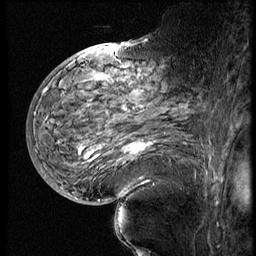
Breast MRI (dynamic contrast-enhanced), one sagittal slice. 4 images stored at this slice position (order not interpretable as contrast timing). 1.5 T. TE 4.2 ms, TR 9 ms. 2.5 mm slice thickness. 256 × 256 image matrix. Female patient, age 56 years. From the clinical record (not read from this slice): setting: breast cancer imaged before/during neoadjuvant chemotherapy; receptor status: HER2-positive.
Annotated regions visible in this slice (semi-automatically segmented with operator editing):
- analysis volume of interest (the breast-tissue region the enhancement analysis was run in; not a lesion): bounding box [x1, y1, x2, y2] px = [82, 83, 199, 177]
- tumour enhancement mask (voxels above the 140 % enhancement threshold inside the analysis volume of interest): [126, 141, 153, 154]